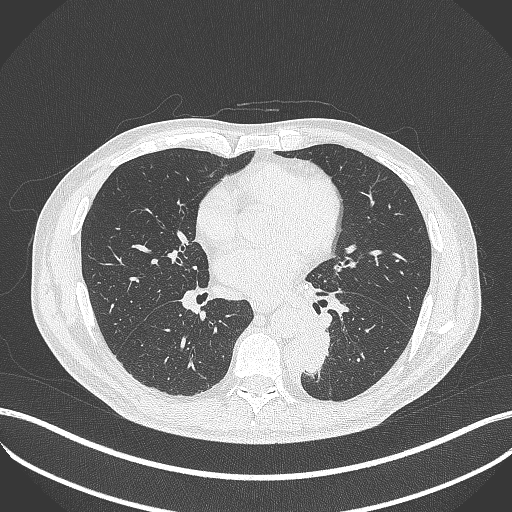
Chest CT, one axial slice. Lung window (W 1500 / L -600 HU). 1 mm slice thickness. 512 × 512 image matrix, field of view 400 × 400 mm. Male patient, age 72 years. From the clinical record (not read from this slice): clinical TNM (as recorded): T2b N0 M1.
Annotated regions visible in this slice (rectangle marked by the reading radiologist):
- lung tumour (recorded histology: adenocarcinoma): bounding box (x1, y1, x2, y2) in pixels: (303, 326, 337, 382)